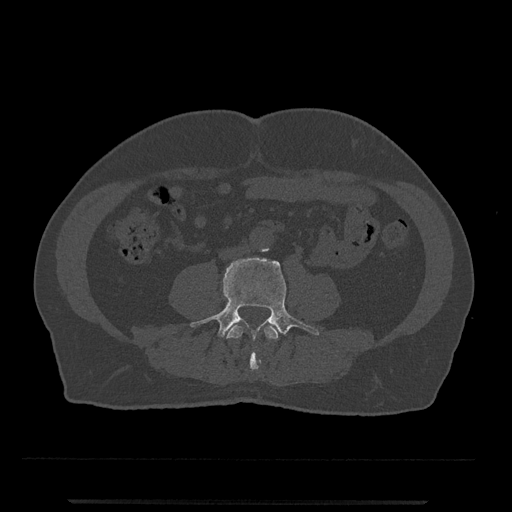
CT including the spine, one axial slice; reconstruction kernel Br40s/3; bone window (W 1800 / L 400 HU); 0.5 mm slice thickness; 512 × 512 image matrix, field of view 419 × 419 mm. Male patient, age 63 years. Case-level facts recorded for this patient, not image findings: primary cancer: prostate.
Annotated regions visible in this slice (semi-automatic segmentation, software-assisted and operator-edited):
- L3 vertebra: bounding box [x1, y1, x2, y2] px = [226, 324, 280, 372]
- L4 vertebra: [190, 257, 319, 364]